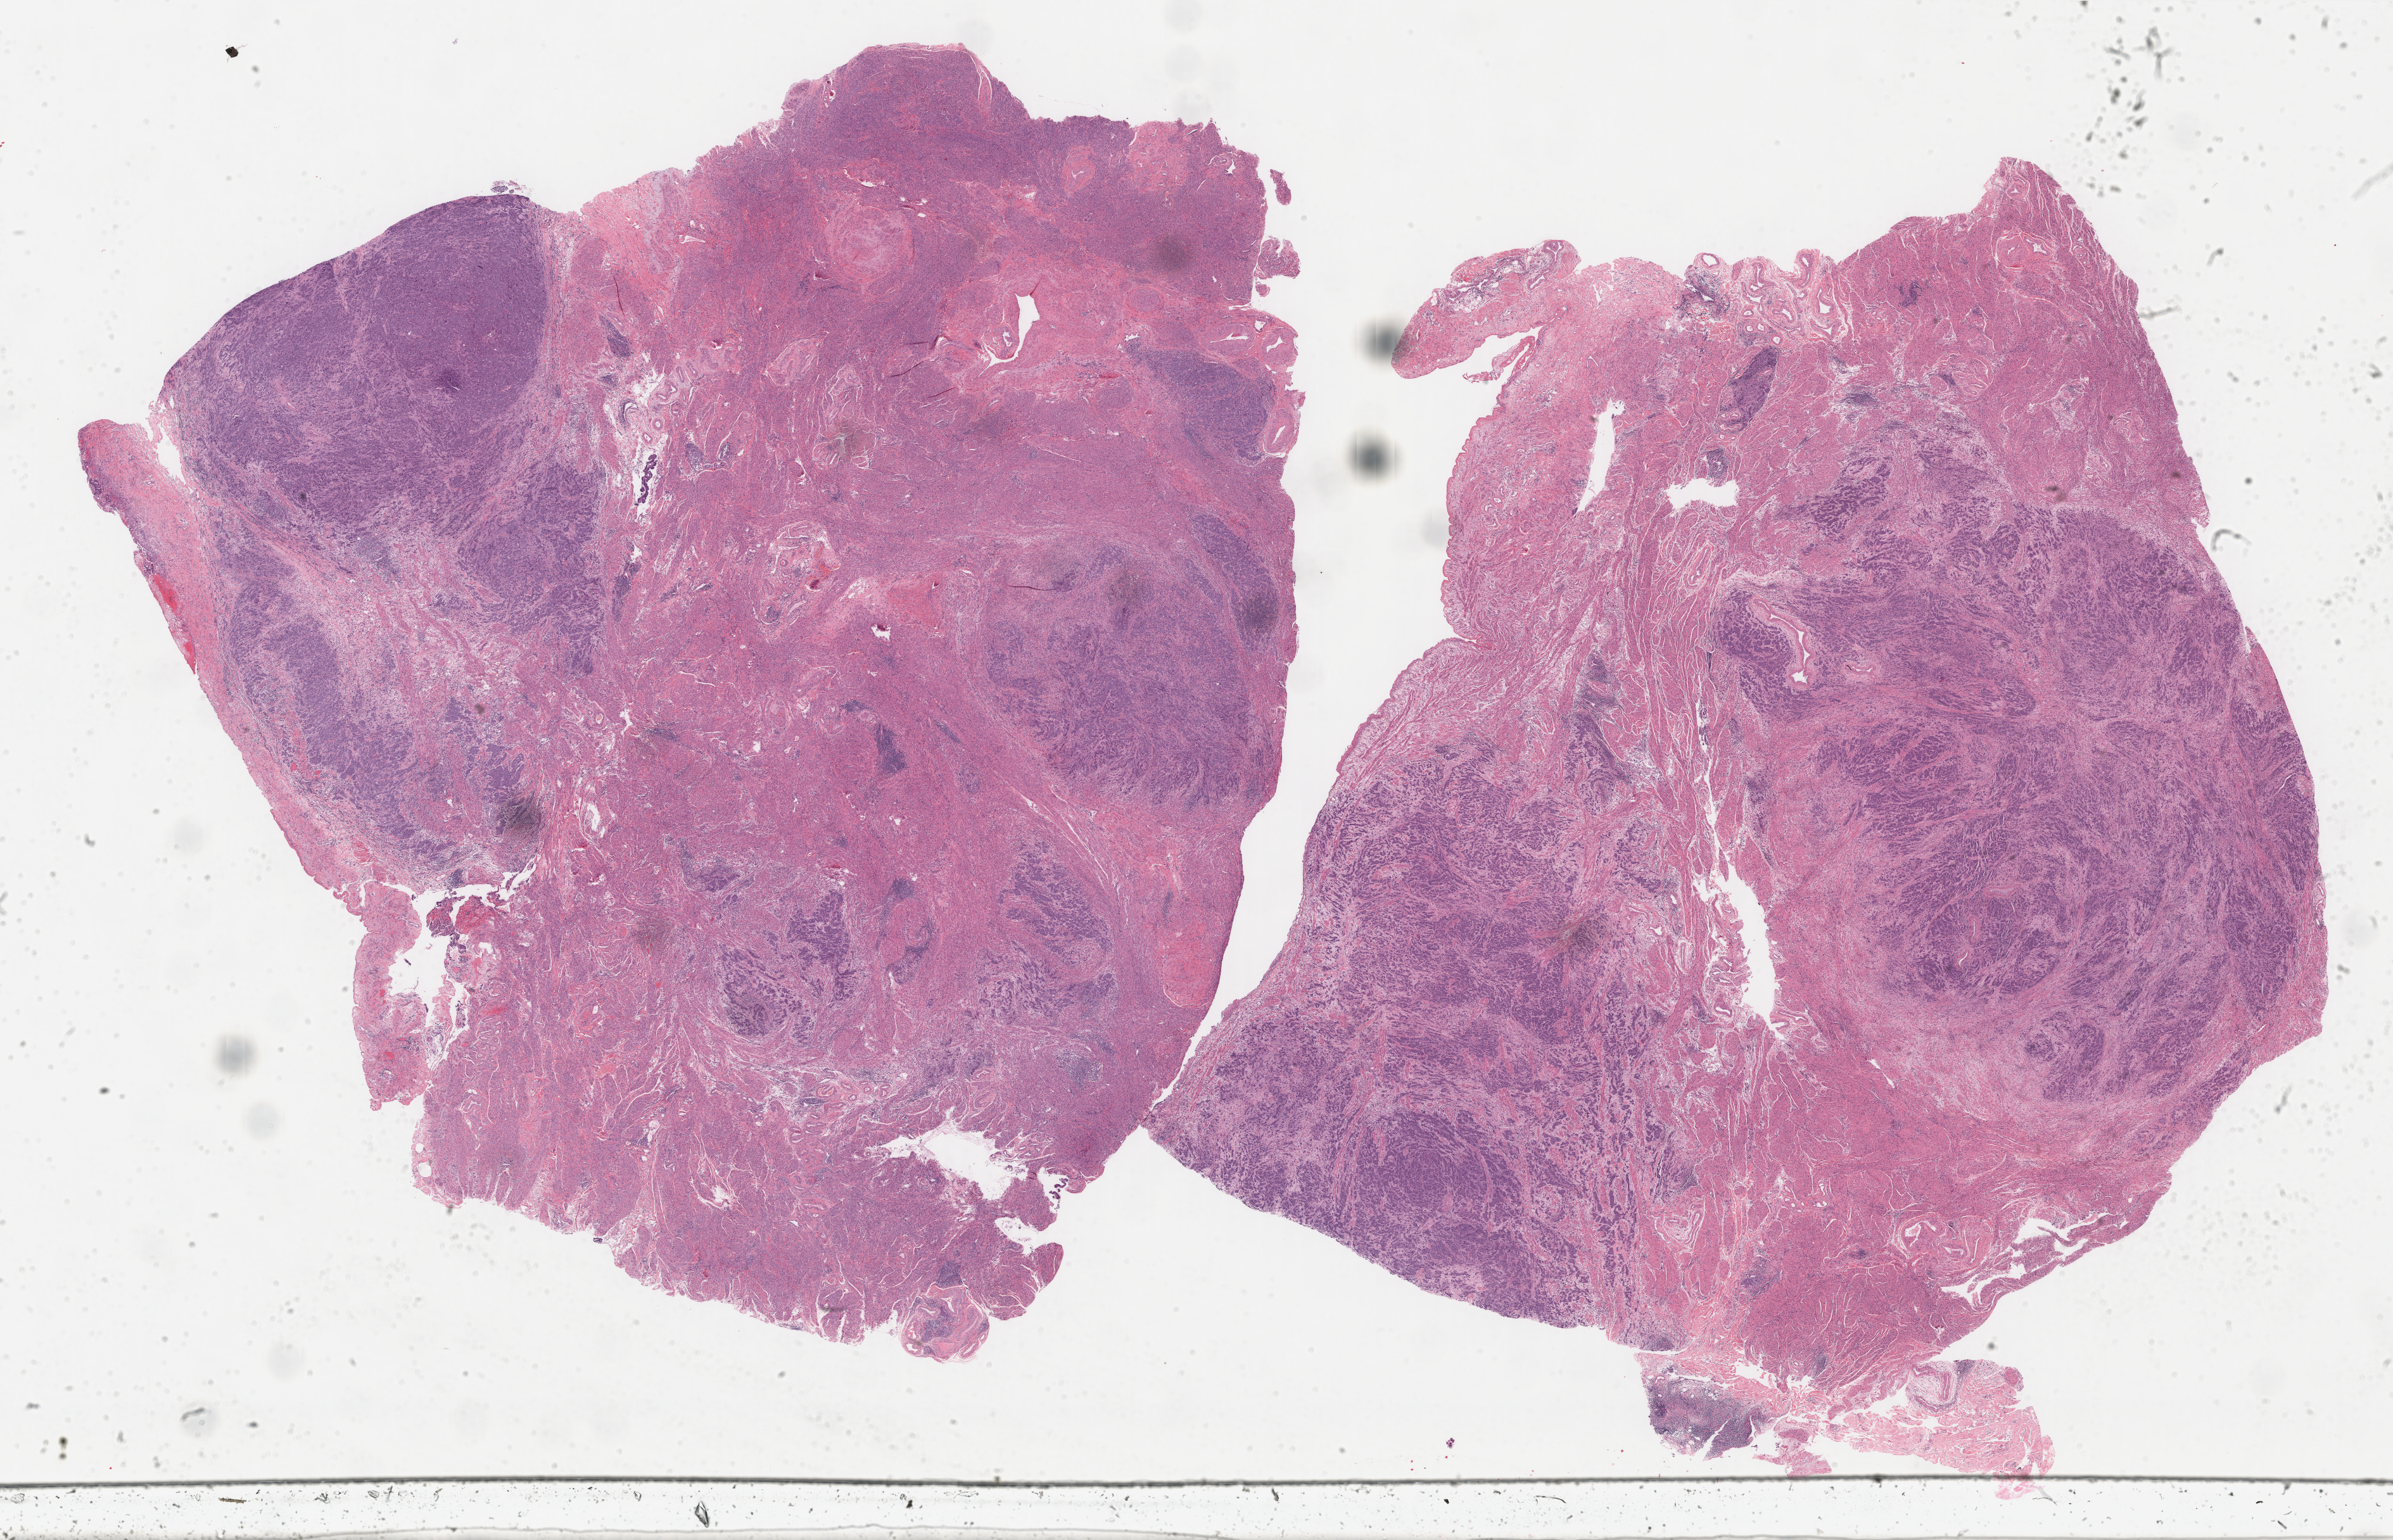
Whole-slide histology image, Hematoxylin and eosin (H&E) stained, shown as a low-resolution overview of the whole scanned area (about 30.0 x 19.3 mm, from a 40x scan). Formalin-fixed paraffin-embedded (FFPE) diagnostic section. Uterus, primary tumour sample. Female patient; age at initial diagnosis 74 years. Histologic grade: high grade.
Lymph nodes positive (case pathology): 0 of 15 examined. Pathologic diagnosis: Serous cystadenocarcinoma, NOS (endometrium). FIGO stage: IV.